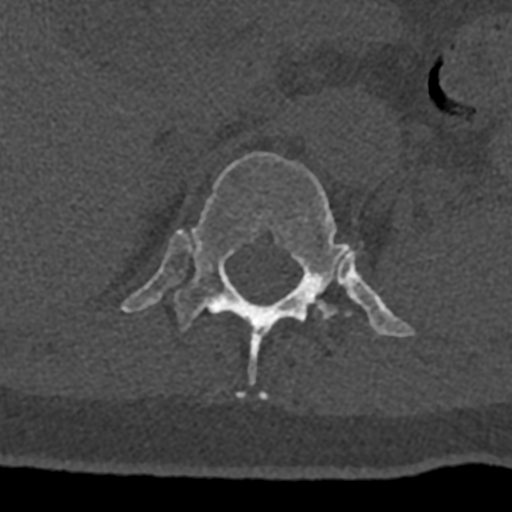
CT including the spine, one axial slice. Position 495 of 797 along the scan axis. Bone window (W 1800 / L 400 HU). 0.5 mm slice thickness. 512 × 512 image matrix, field of view 160 × 160 mm. Patient: male, 74 years. From the clinical record (not read from this slice): primary cancer: renal; vertebrae with lytic lesions (as recorded): T10, L1, L2, L3, L4, L5.
Outlined on this slice (semi-automatically segmented with operator editing):
- T12 vertebra: bounding box (x1, y1, x2, y2) in pixels: (121, 151, 414, 398)